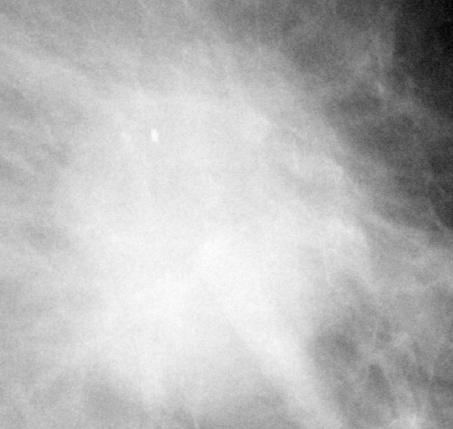
Cropped region of a digitized screen-film mammogram centred on a radiologist-marked abnormality; left breast; CC view.
Marked abnormality: mass, shape irregular, margins ill defined / spiculated; BI-RADS assessment category 4; subtlety rating 5 on a 1 (subtle) to 5 (obvious) scale; pathology (as recorded): malignant.